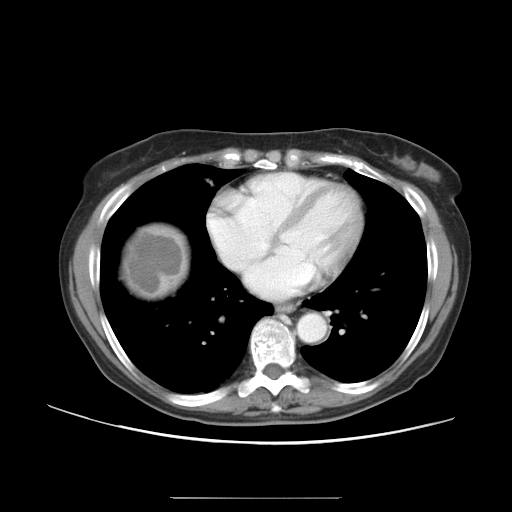
Contrast-enhanced abdominal CT, one axial slice; position 47 of 50 along the scan axis; reconstruction kernel STANDARD; 120 kVp; intravenous contrast given; soft-tissue window (W 400 / L 40 HU); 5 mm slice thickness; 512 × 512 image matrix, field of view 389 × 389 mm. Female patient, age 58 years. Case-level facts recorded for this patient, not image findings: diagnosis: colorectal cancer liver metastases, imaged before liver resection; multiple liver metastases: yes; largest metastasis: 7.3 cm.
Structures marked on this image (outlined manually by an expert reader):
- liver: bounding box <123,227,185,297> (left, top, right, bottom; pixels)
- liver metastasis: <128,232,182,296>